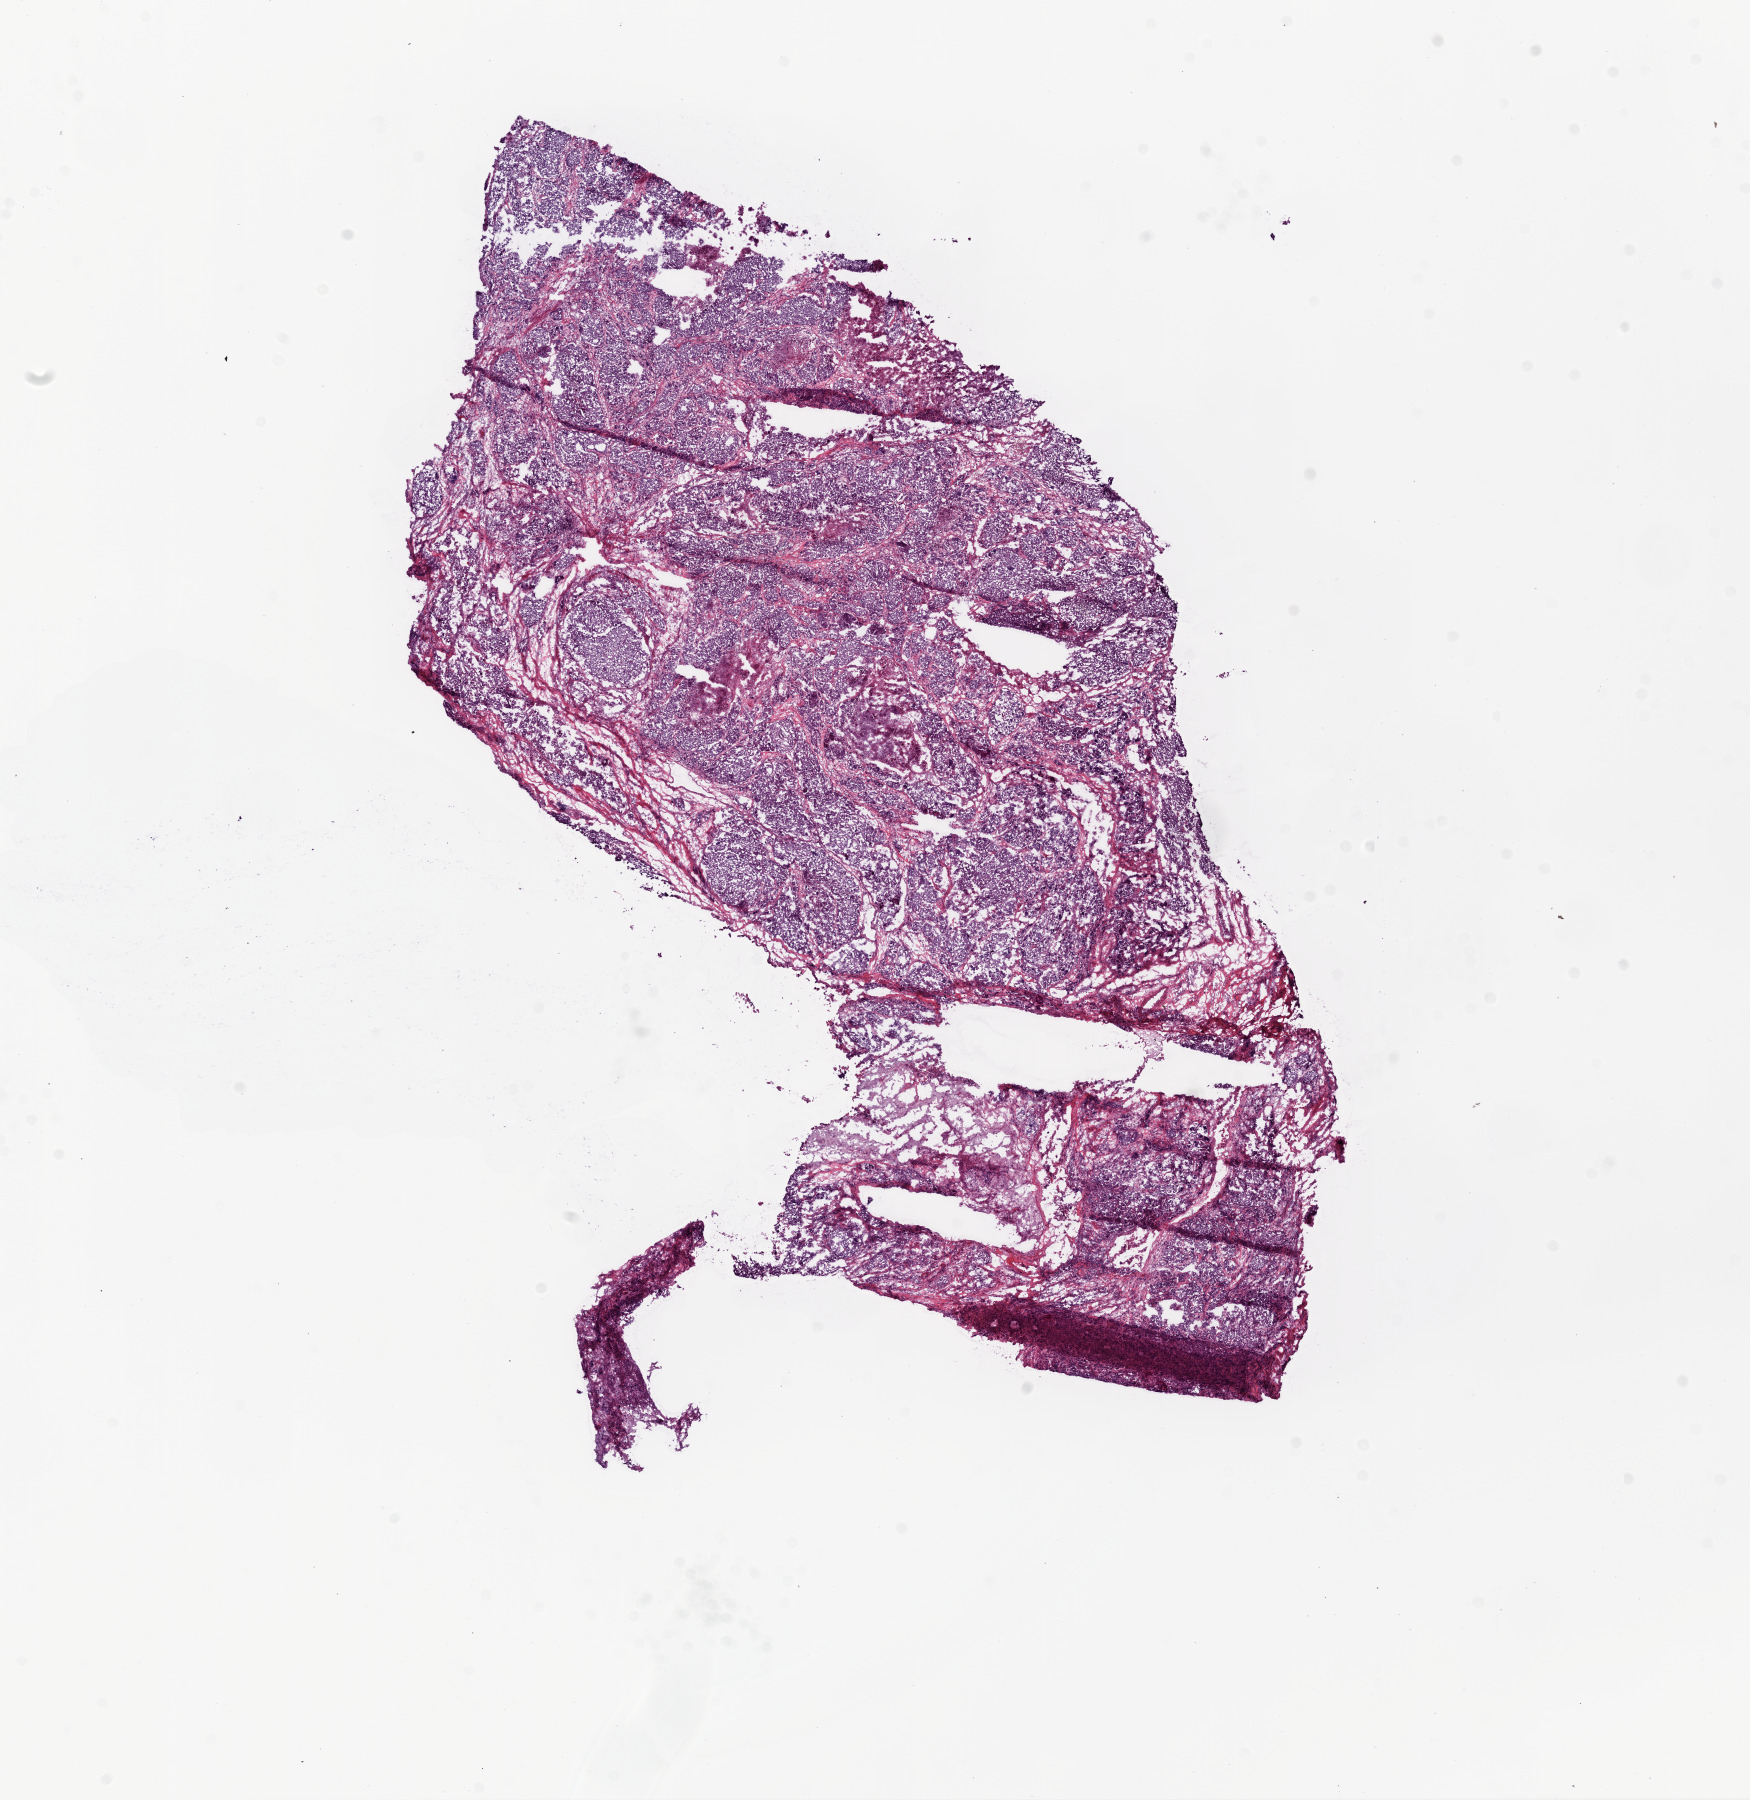
Whole-slide histology image, Hematoxylin and eosin (H&E) stained, whole scanned area (about 14.0 x 14.4 mm) shown as a low-resolution overview. Frozen section from the top of the tissue portion. Ovary, primary tumour sample. Female patient; age at initial diagnosis 57 years. Histologic grade: G3 (poorly differentiated). Slide review estimates, as recorded: tumour cells 75%, tumour nuclei 90%, normal cells 1%, stromal cells 9%, necrosis 15%.
Pathologic diagnosis: Serous cystadenocarcinoma, NOS. FIGO stage: IIIC.